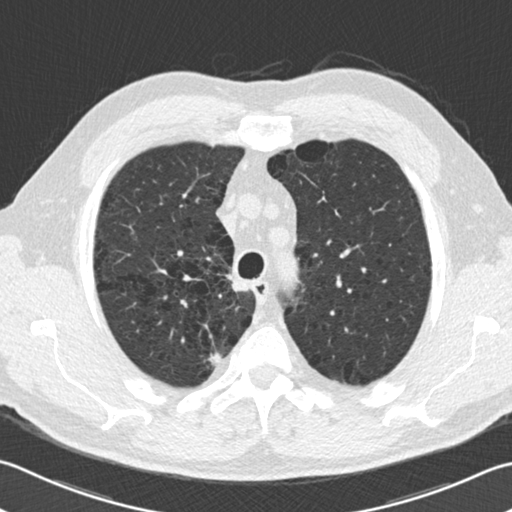
Low-dose screening chest CT, axial slice. Second annual screen. Lung window (W 1500 / L -600 HU). Slice 46 of 206 in the series. 512 × 512 image matrix, field of view 346 × 346 mm. Male participant, aged 68 years at enrolment. Current smoker at enrolment.
Expert-annotated lung lesion, bounding box [x1, y1, x2, y2] px = [195, 340, 235, 377]. The exam's reader record, not a measurement of the box and not confirmed to be the same lesion: non-calcified nodule or mass ≥4 mm, right upper lobe, 30 × 20 mm, smooth margins, pre-existing on the prior screen: no.